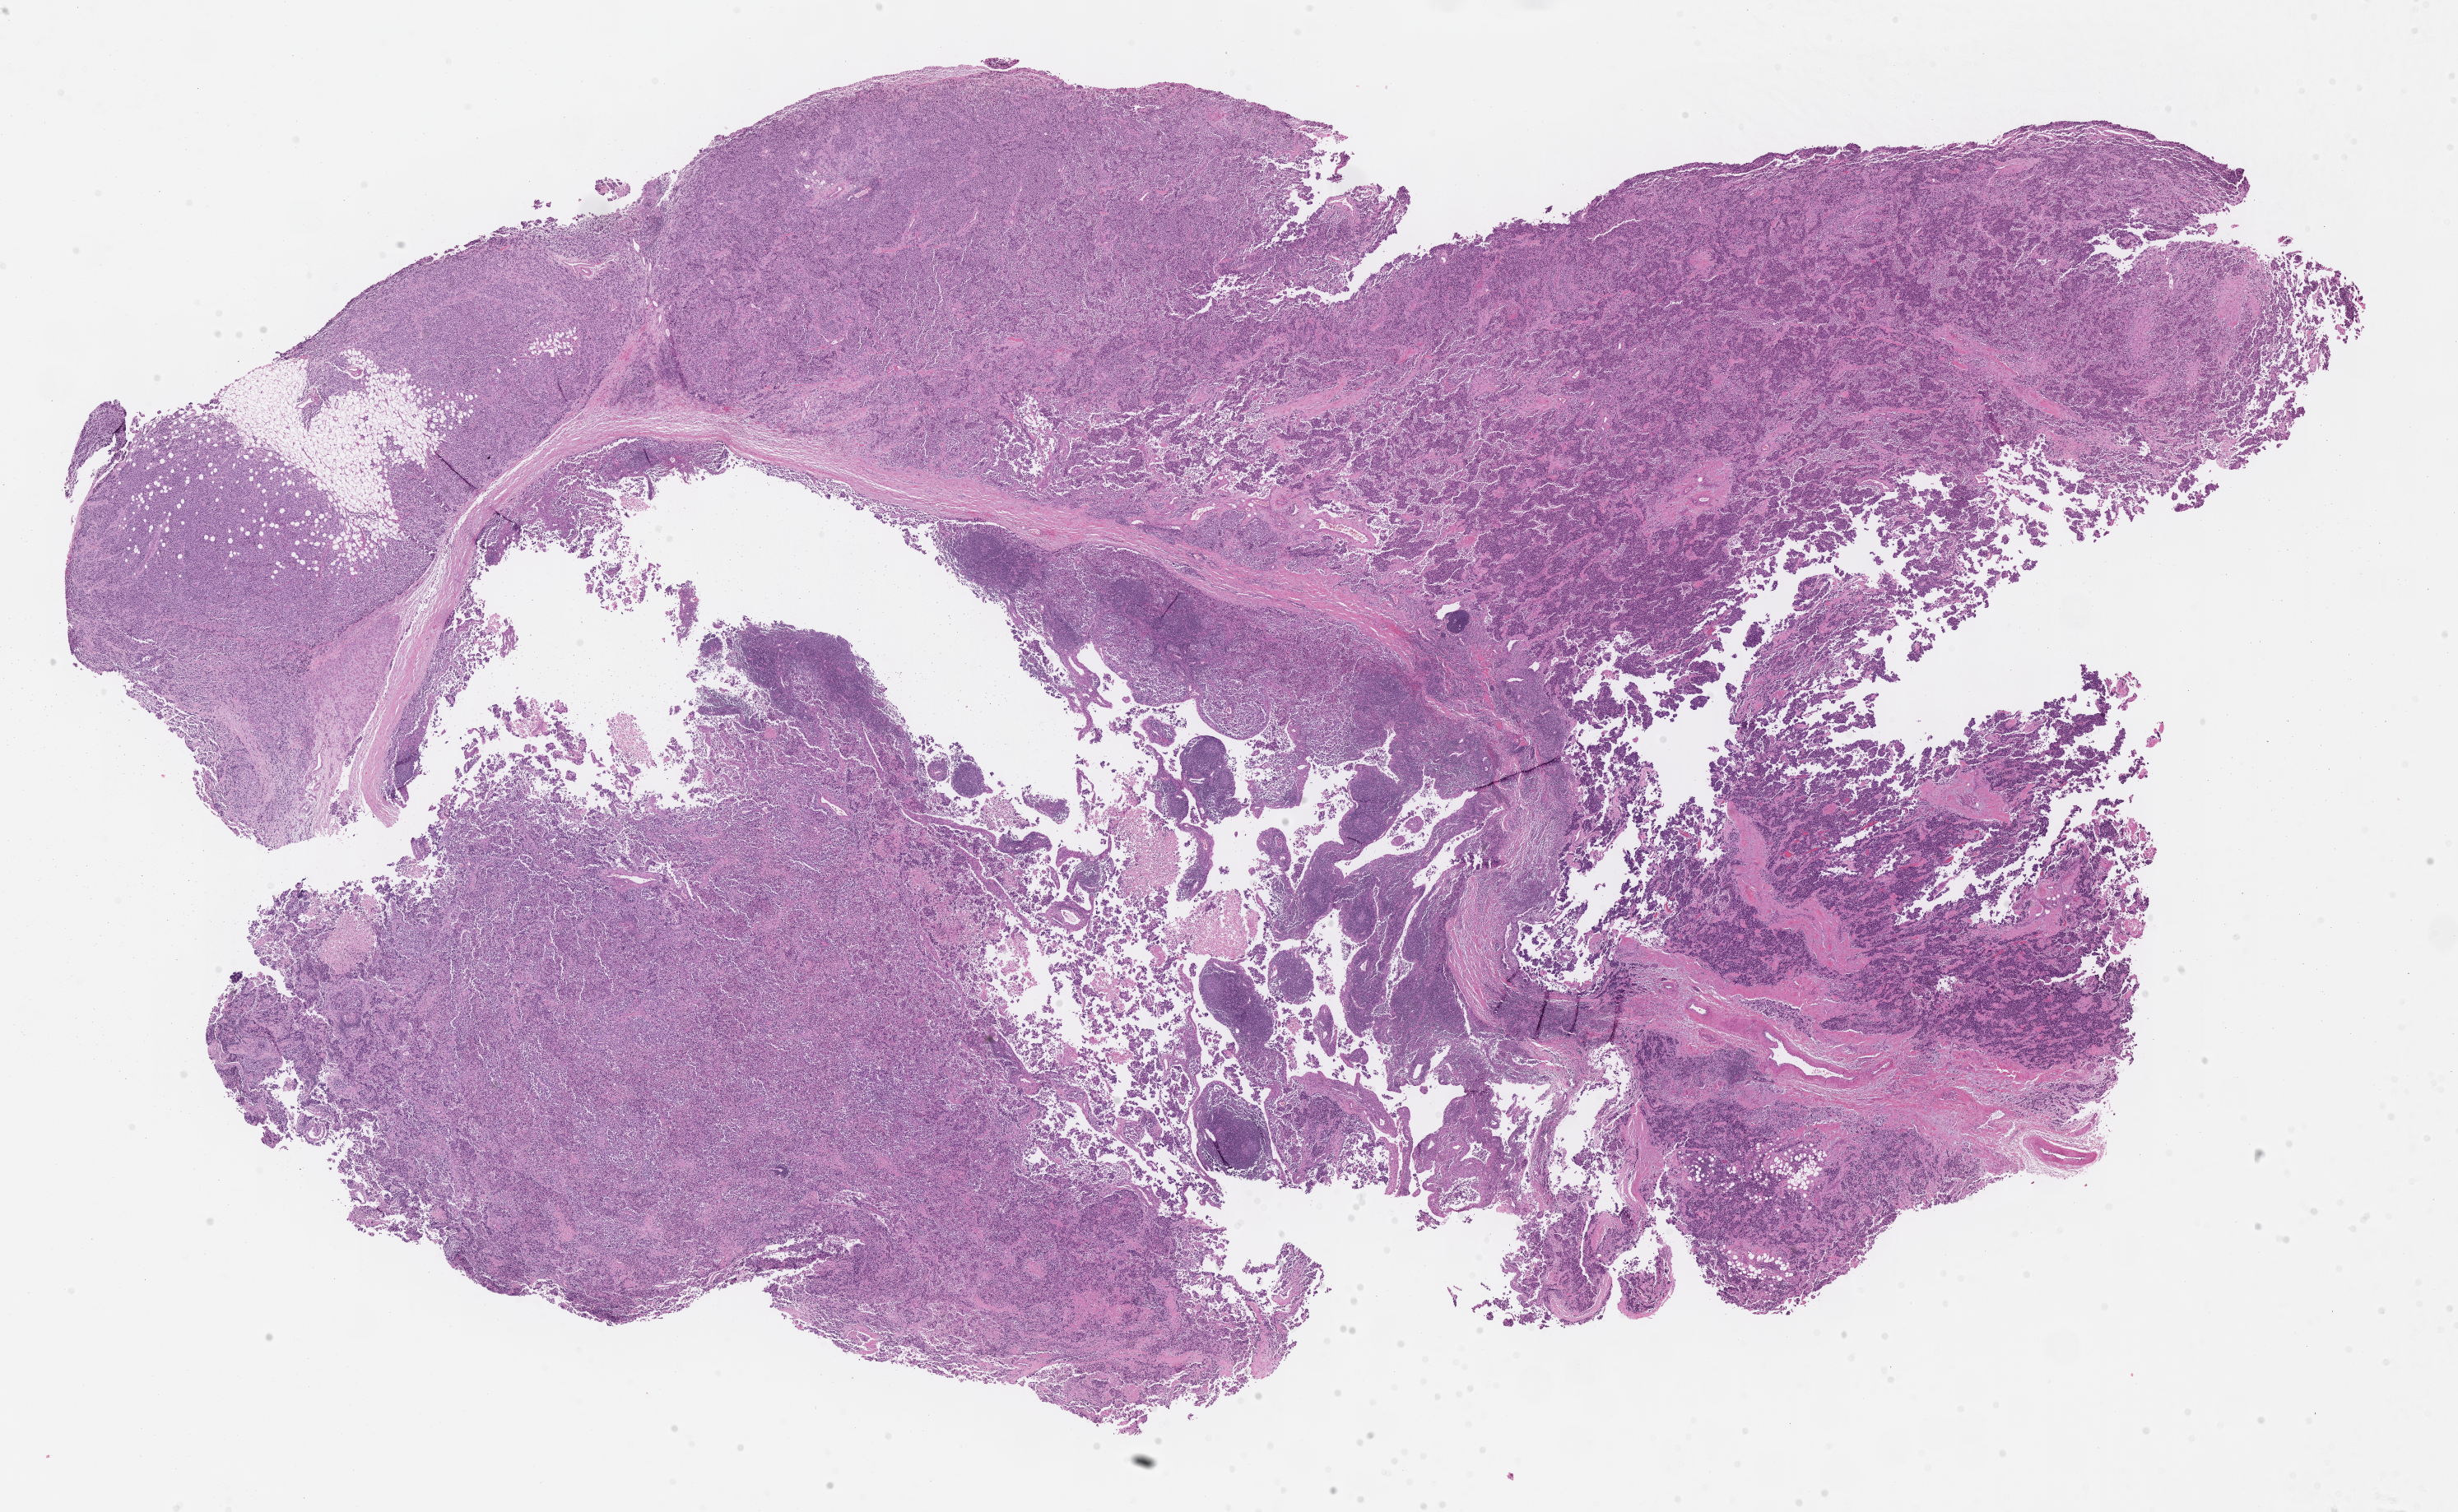
Whole-slide image, H&E stain of tumor tissue — shown as a low-resolution overview of the whole scanned area (about 24.2 x 14.9 mm), FFPE section, sample anatomic site: lymph node. Male patient, age at diagnosis 10.5 years.
Stage (as recorded): 4. Diagnosis: rhabdomyosarcoma; histological classification: alveolar rhabdomyosarcoma. Primary site (case record): forearm. Metastatic status at presentation (as recorded): metastatic (confirmed).